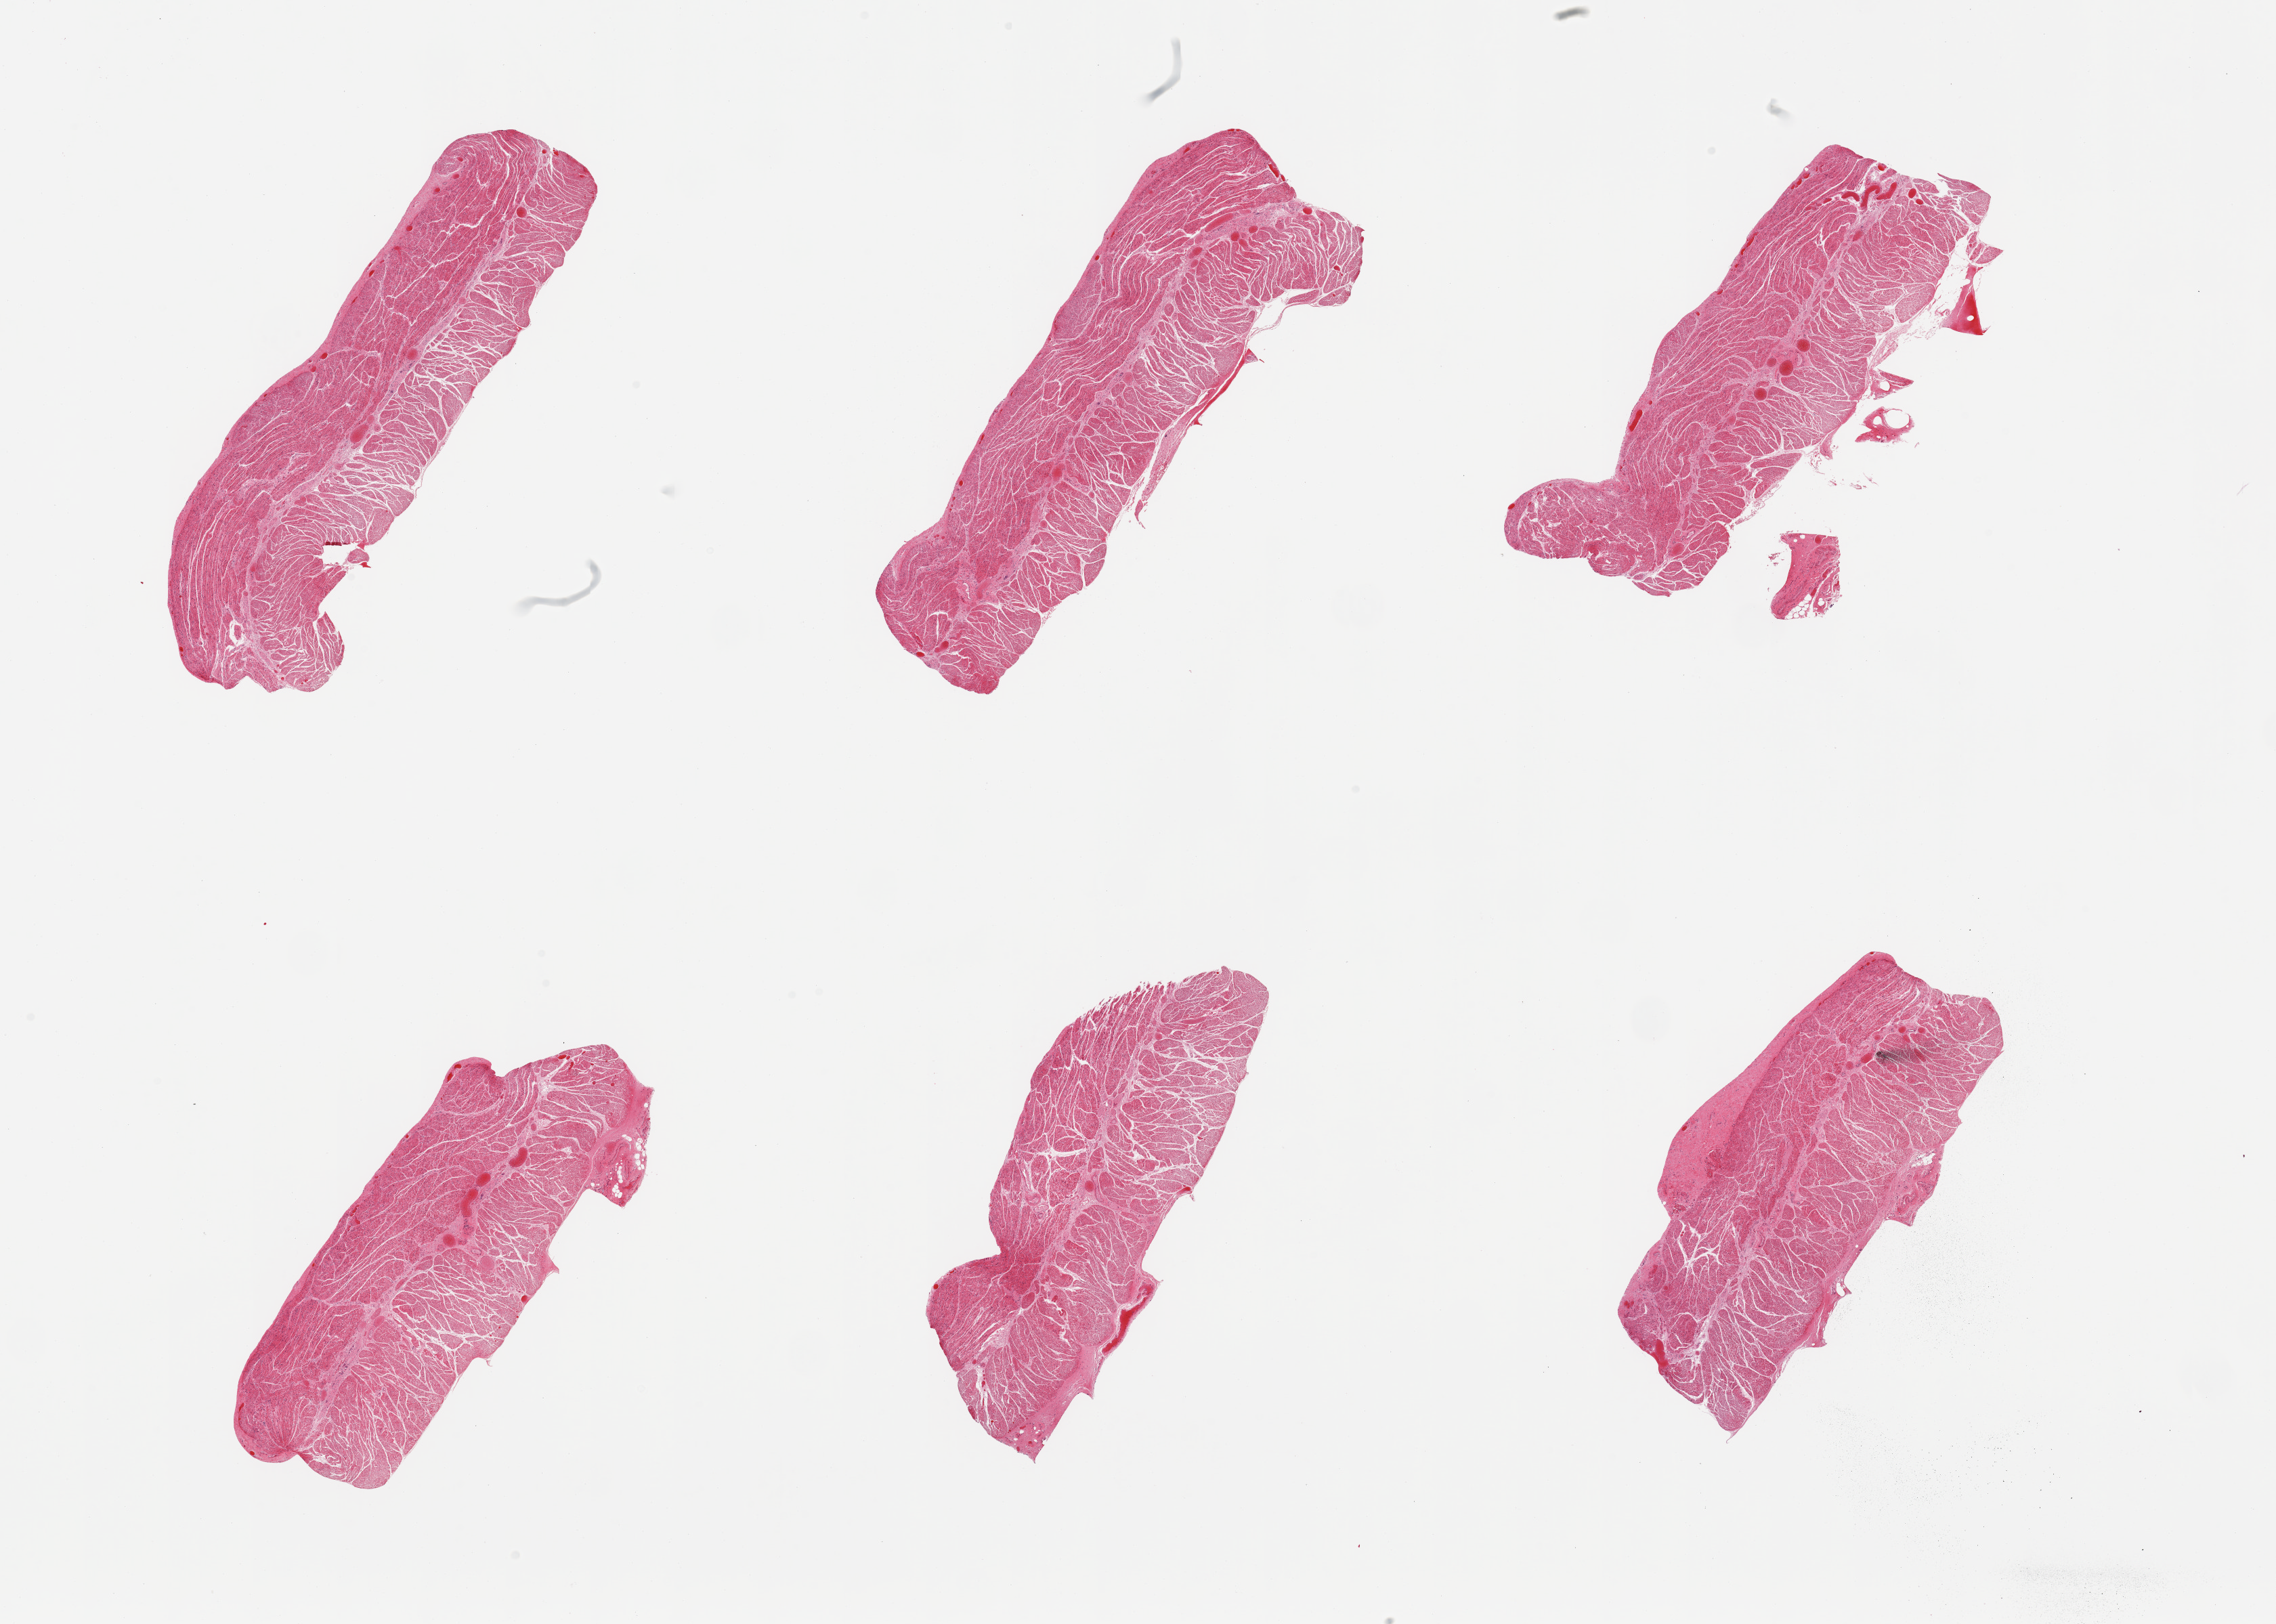
Whole-slide image, haematoxylin and eosin stain — a low-resolution overview of the entire scanned area, about 26.6 x 19.0 mm (from a 20x scan); PAXgene-fixed paraffin-embedded (PFPE) section; sampled site (target tissue): esophageal muscle; tissue donor sample. Donor: male.
- review note (as recorded): 6 pieces; well trimmed